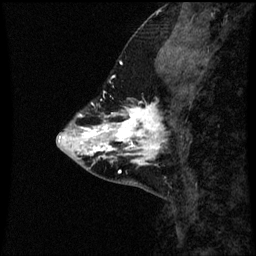
Breast MRI (dynamic contrast-enhanced), one sagittal slice. Slice 18 of 60 in the series (ordered by position). Dynamic contrast-enhanced series, image 2 of 3 at this slice position (ordered by acquisition). 1.5 T. TE 4.2 ms, TR 8.9 ms. 2 mm slice thickness. 256 × 256 image matrix, field of view 200 × 200 mm. Female patient, age 43 years. Case-level facts recorded for this patient, not image findings: setting: breast cancer imaged before/during neoadjuvant chemotherapy; receptor status: HR-positive, HER2-negative.
Structures marked on this image (semi-automatic segmentation, software-assisted and operator-edited):
- analysis volume of interest (the breast-tissue region the enhancement analysis was run in; not a lesion): bounding box (x1, y1, x2, y2) in pixels: (110, 102, 164, 163)
- tumour enhancement mask (voxels above the 70 % enhancement threshold inside the analysis volume of interest): (110, 102, 164, 163)